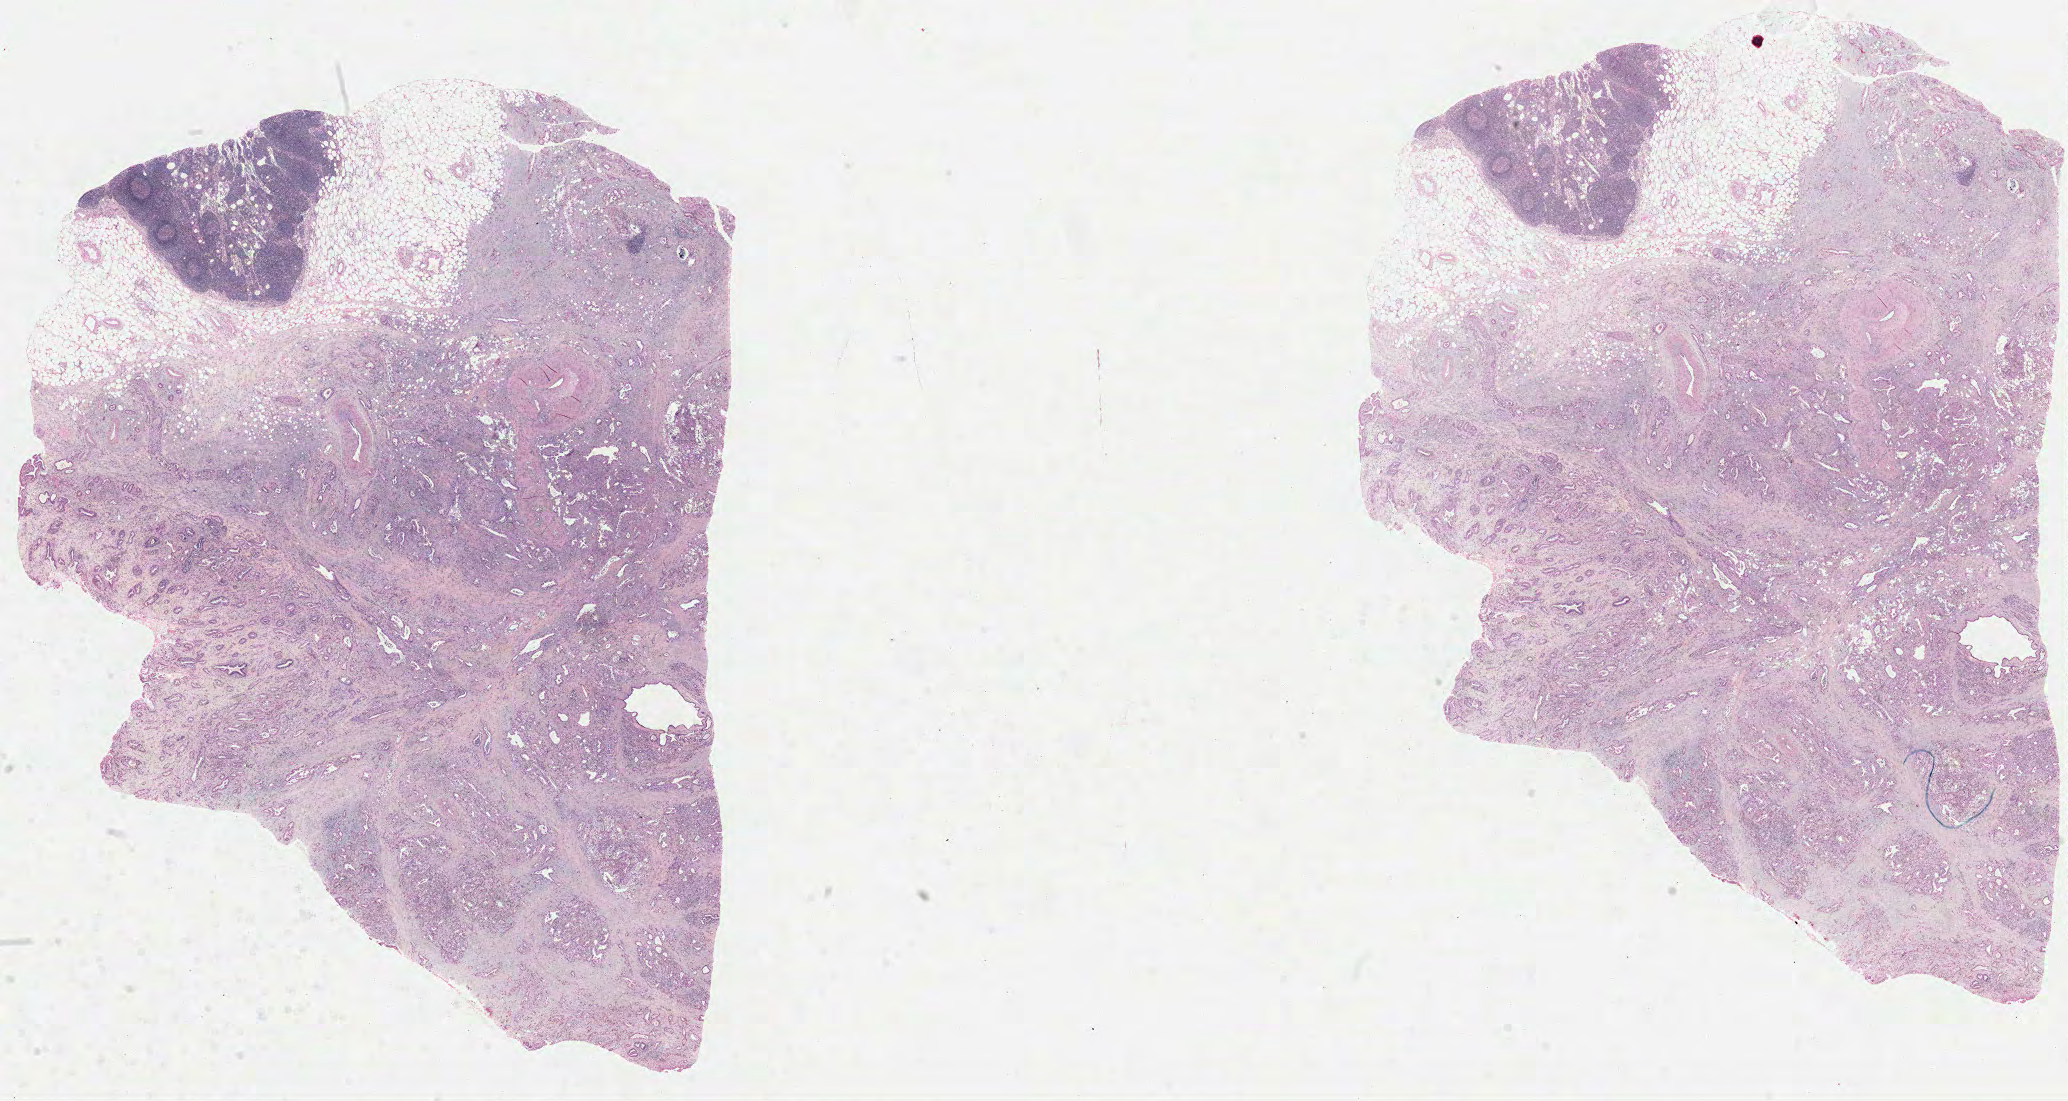
Whole-slide histology image, Hematoxylin and eosin (H&E) stained, low-resolution overview of the scanned area, about 33.4 x 17.8 mm (from a 40x scan). FFPE section. Pancreas, primary tumour sample. Male patient; age at initial diagnosis 70 years. Histologic grade: G1 (well differentiated).
Lymph nodes positive (case pathology): 1 of 9 examined. AJCC pathologic stage: IIB. Diagnosis: Adenocarcinoma, NOS (head of pancreas).